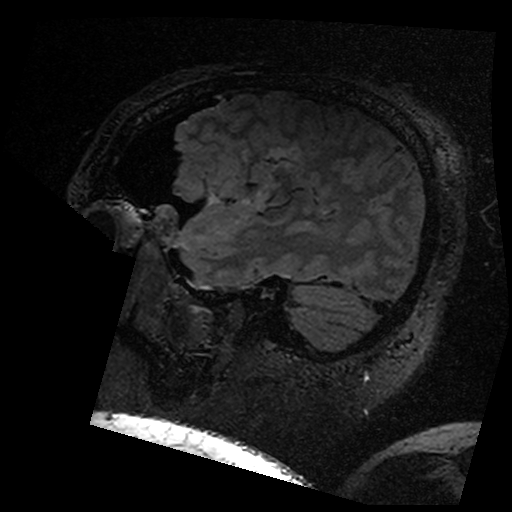
Brain MRI from a brain-tumour surgery series, one sagittal slice; slice 133 of 176 in the series (ordered by position); T2 FLAIR; 1 mm slice thickness; 512 × 512 image matrix, field of view 250 × 250 mm. From the clinical record (not read from this slice): histopathology: Astrocytoma; WHO grade: 3.
Annotated regions visible in this slice (outlined manually by an expert reader):
- residual tumour: bounding box (x1, y1, x2, y2) in pixels: (278, 156, 290, 163)